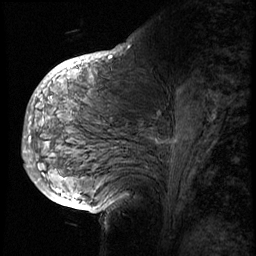
Breast MRI (dynamic contrast-enhanced), one sagittal slice. 3 images stored at this slice position (order not interpretable as contrast timing). 1.5 T. TE 4.2 ms, TR 8.9 ms. 256 × 256 image matrix, field of view 220 × 220 mm. Patient: female, 57 years. From the clinical record (not read from this slice): setting: breast cancer imaged before/during neoadjuvant chemotherapy; receptor status: HER2-positive.
Annotated regions visible in this slice (semi-automatic segmentation, software-assisted and operator-edited):
- analysis volume of interest (the breast-tissue region the enhancement analysis was run in; not a lesion): box from (x=28, y=70) to (x=228, y=156) px
- tumour enhancement mask (voxels above the 140 % enhancement threshold inside the analysis volume of interest): (x=30, y=137)–(x=32, y=141)